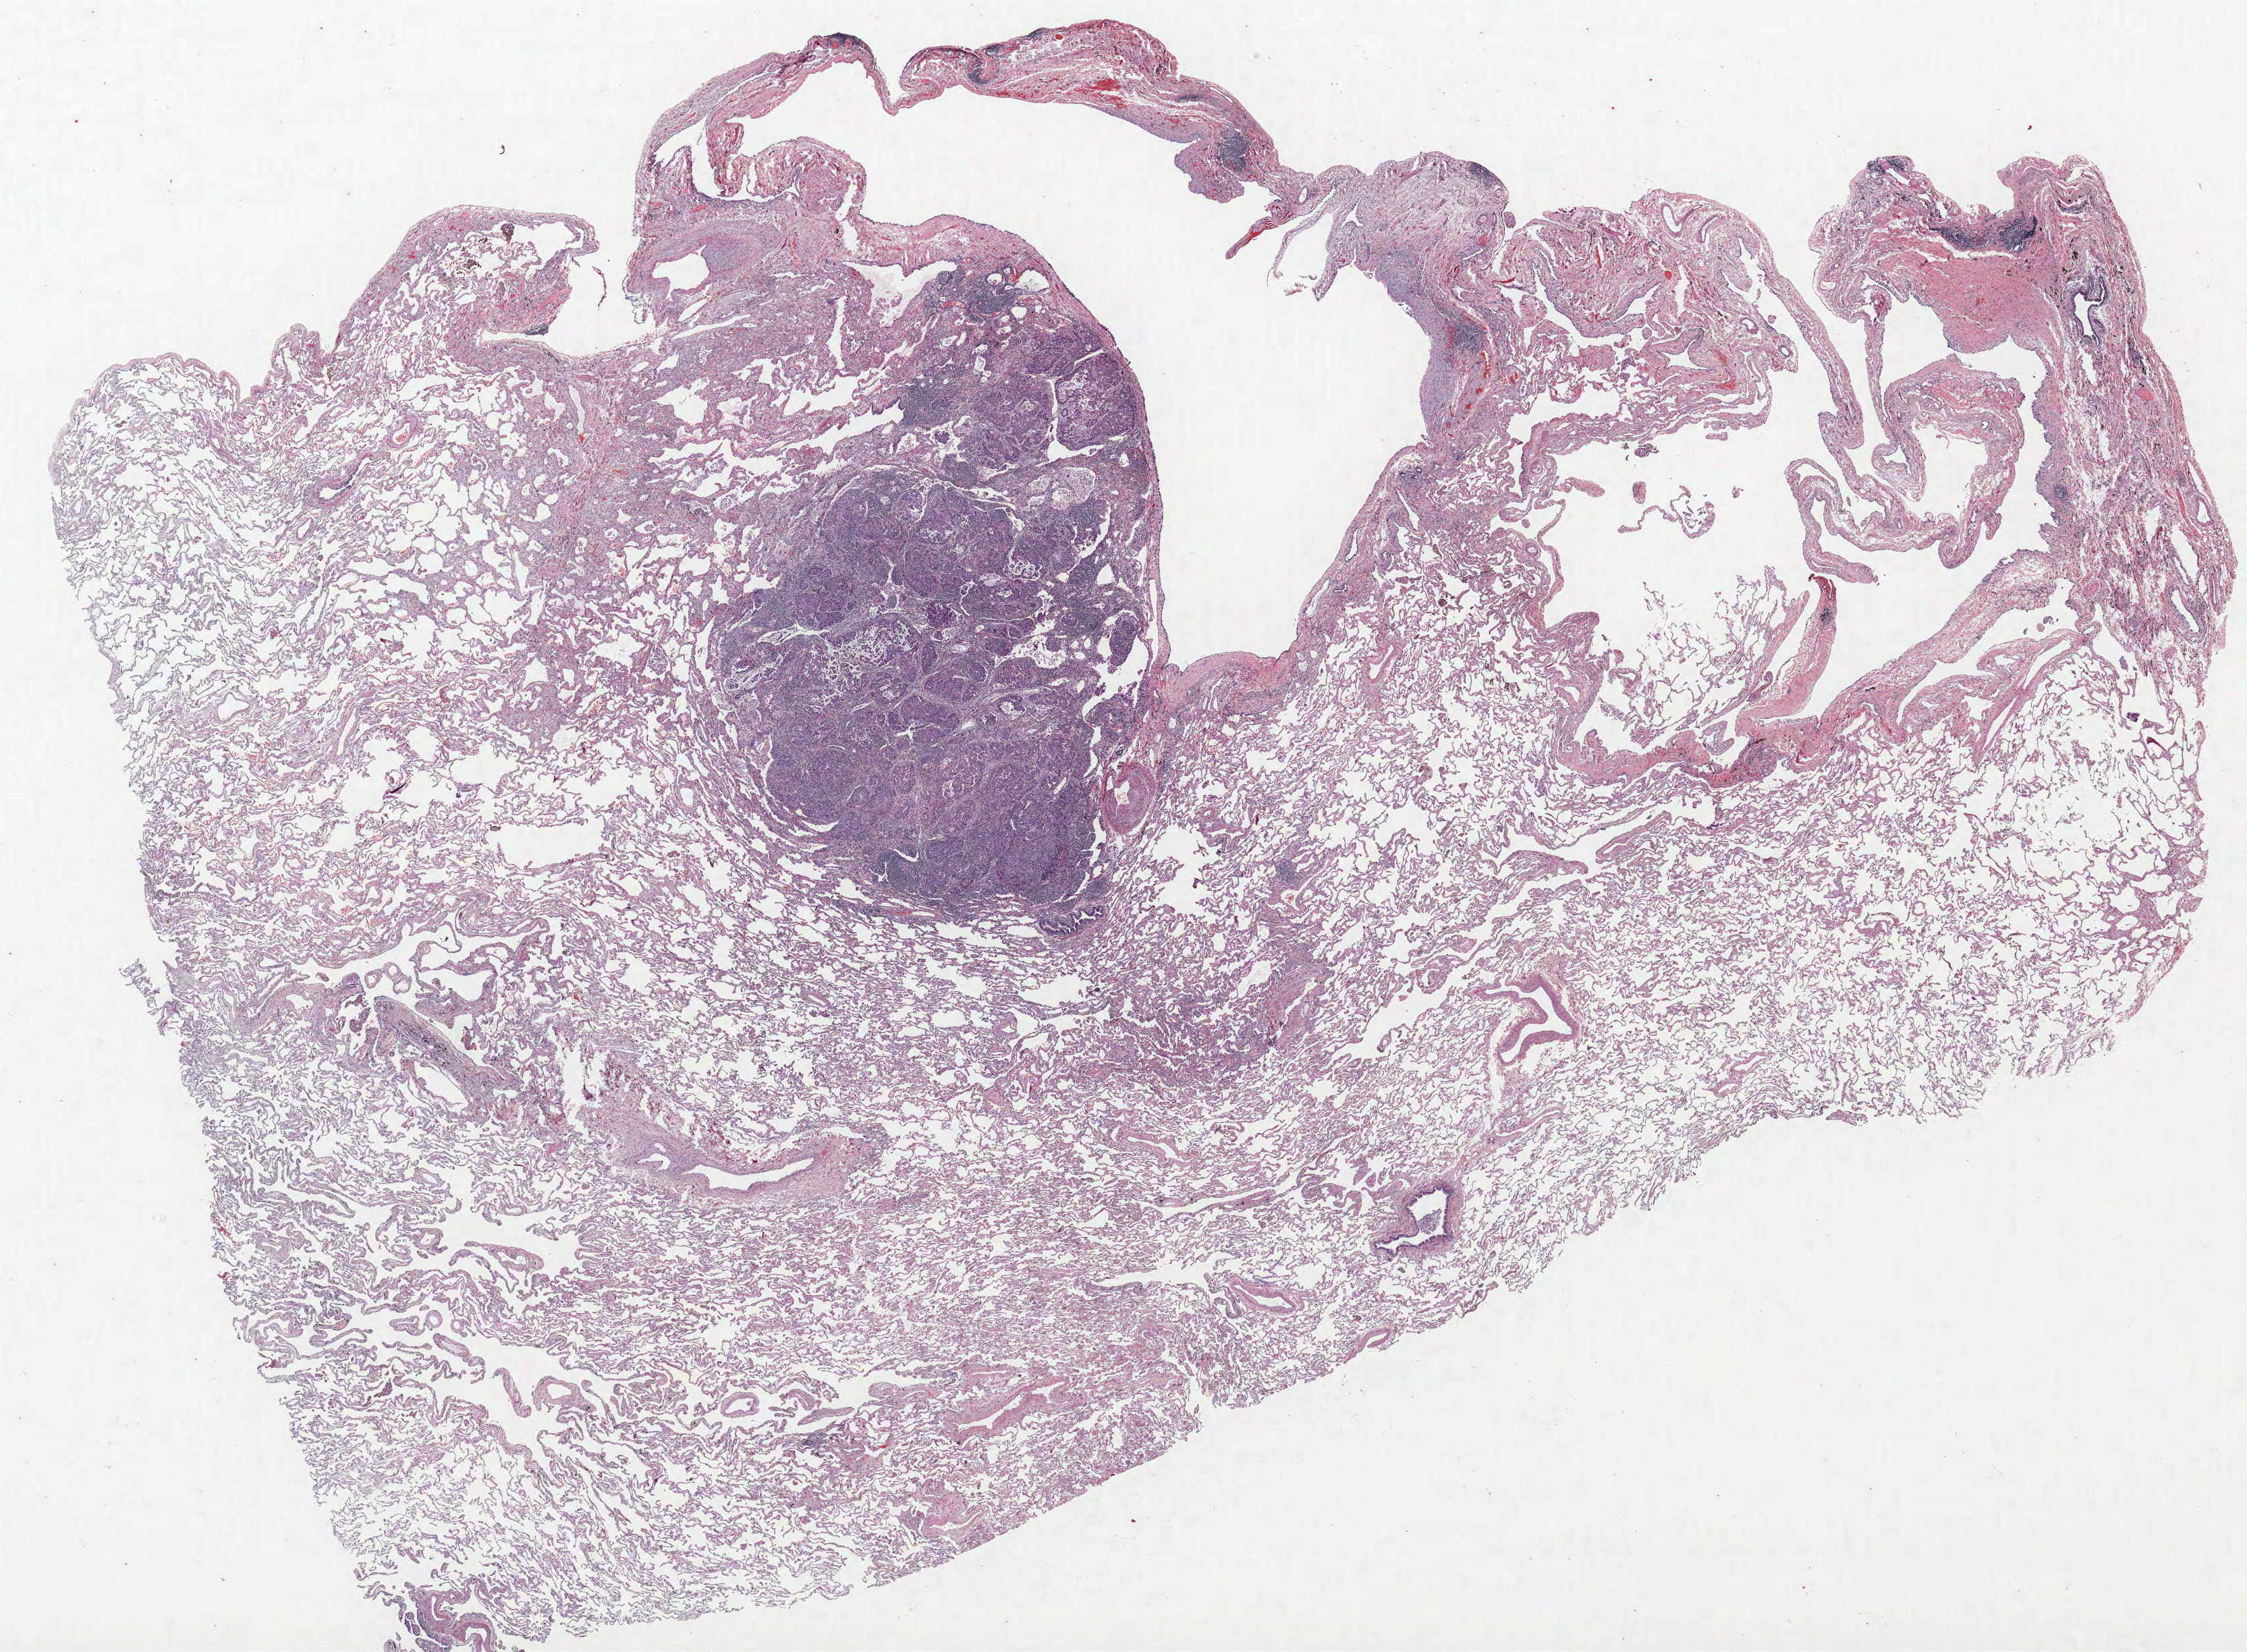
Whole-slide histology image, Hematoxylin and eosin (H&E) stained, whole scanned area (about 26.6 x 19.6 mm, slide scanned at 40x) shown as a low-resolution overview, formalin-fixed paraffin-embedded (FFPE) section, lung. Female, age 64 at enrolment. Grade: poorly differentiated (G3).
* stage (AJCC 6th edition): IB
* primary tumour location (clinical record): right upper lobe
* tumour size (pathology): 15 mm
* participant's lung-cancer diagnosis: Adenocarcinoma, NOS